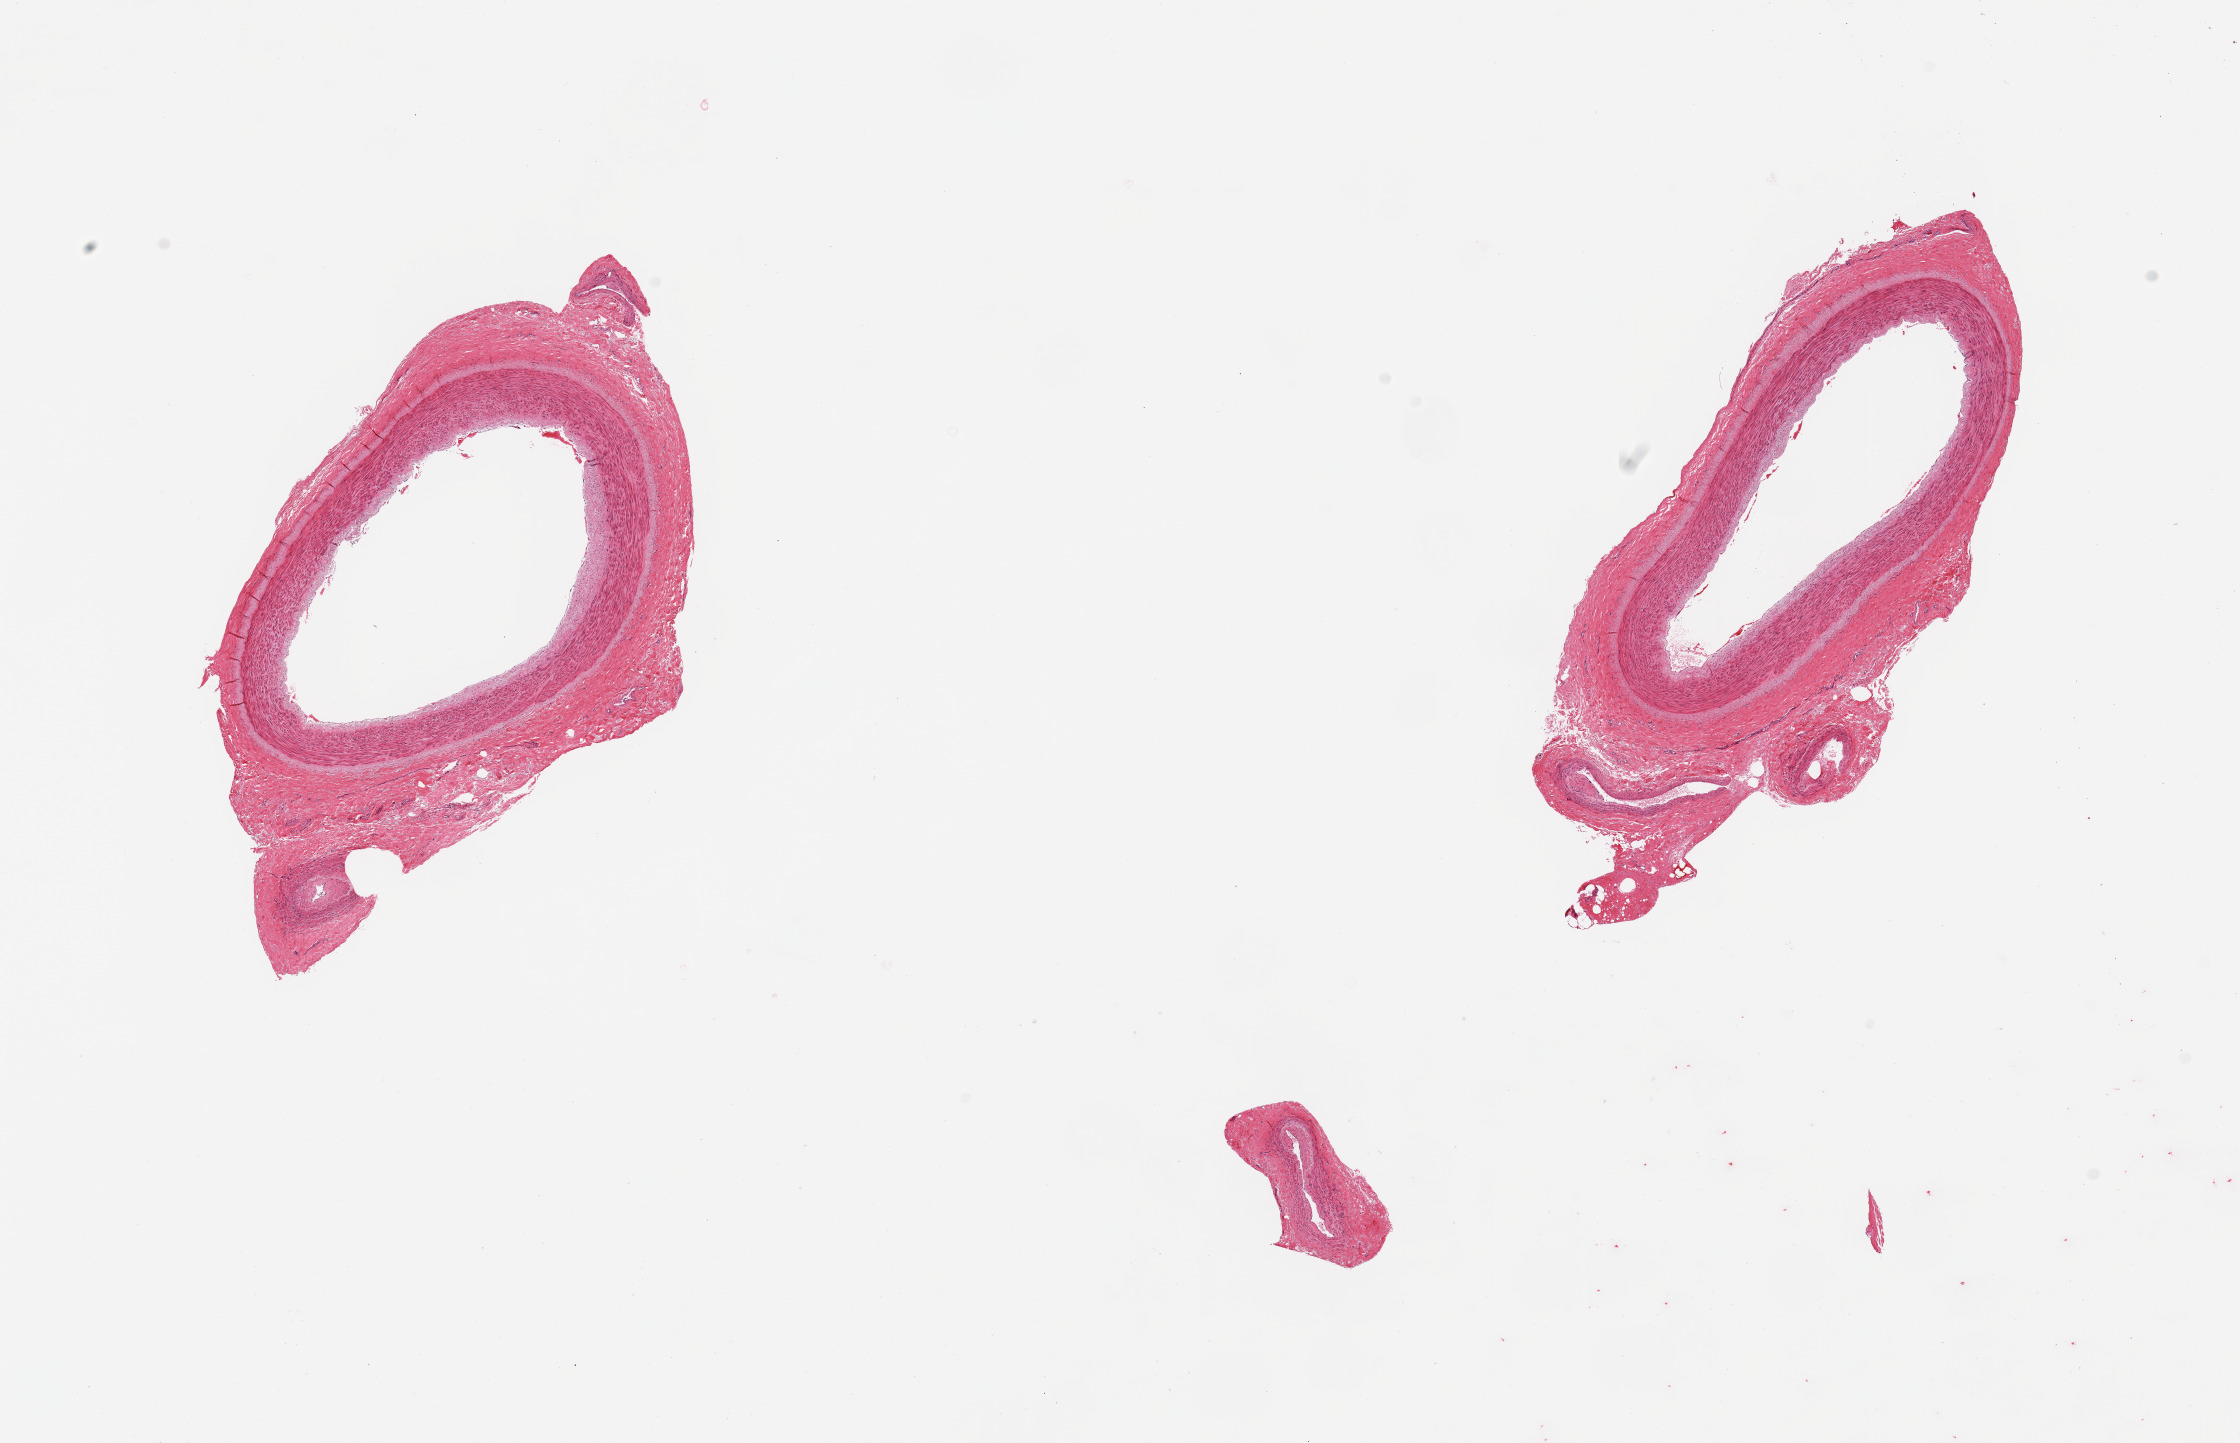
Whole-slide image, H&E stain, low-resolution overview of the scanned area, about 17.7 x 11.4 mm. PAXgene-fixed, paraffin-embedded tissue. Section of tibial artery (target tissue). Tissue donor sample.
- pathologist's review note for this sample: 2 pieces; well trimmed of fat, attached smaller vessels, intimal thickening